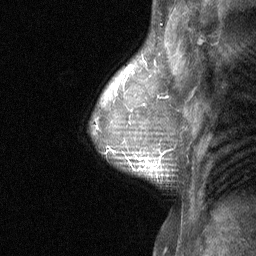
Breast MRI (dynamic contrast-enhanced), one sagittal slice. Slice 48 of 64 in the series (ordered by position). Dynamic contrast-enhanced study with each time point stored as its own series, time point 2 of 3 at this slice position (early post-contrast, ordered by acquisition time). 1.5 T. TE 4.8 ms, TR 27 ms. 2 mm slice thickness. 256 × 256 image matrix, field of view 180 × 180 mm. Patient: female, 47 years. Case-level facts recorded for this patient, not image findings: setting: breast cancer imaged before/during neoadjuvant chemotherapy; receptor status: HR-positive, HER2-negative.
Annotated regions visible in this slice (semi-automatic segmentation, software-assisted and operator-edited):
- analysis volume of interest (the breast-tissue region the enhancement analysis was run in; not a lesion): bounding box (x1, y1, x2, y2) in pixels: (104, 138, 165, 184)
- tumour enhancement mask (voxels above the 90 % enhancement threshold inside the analysis volume of interest): (139, 153, 163, 169)